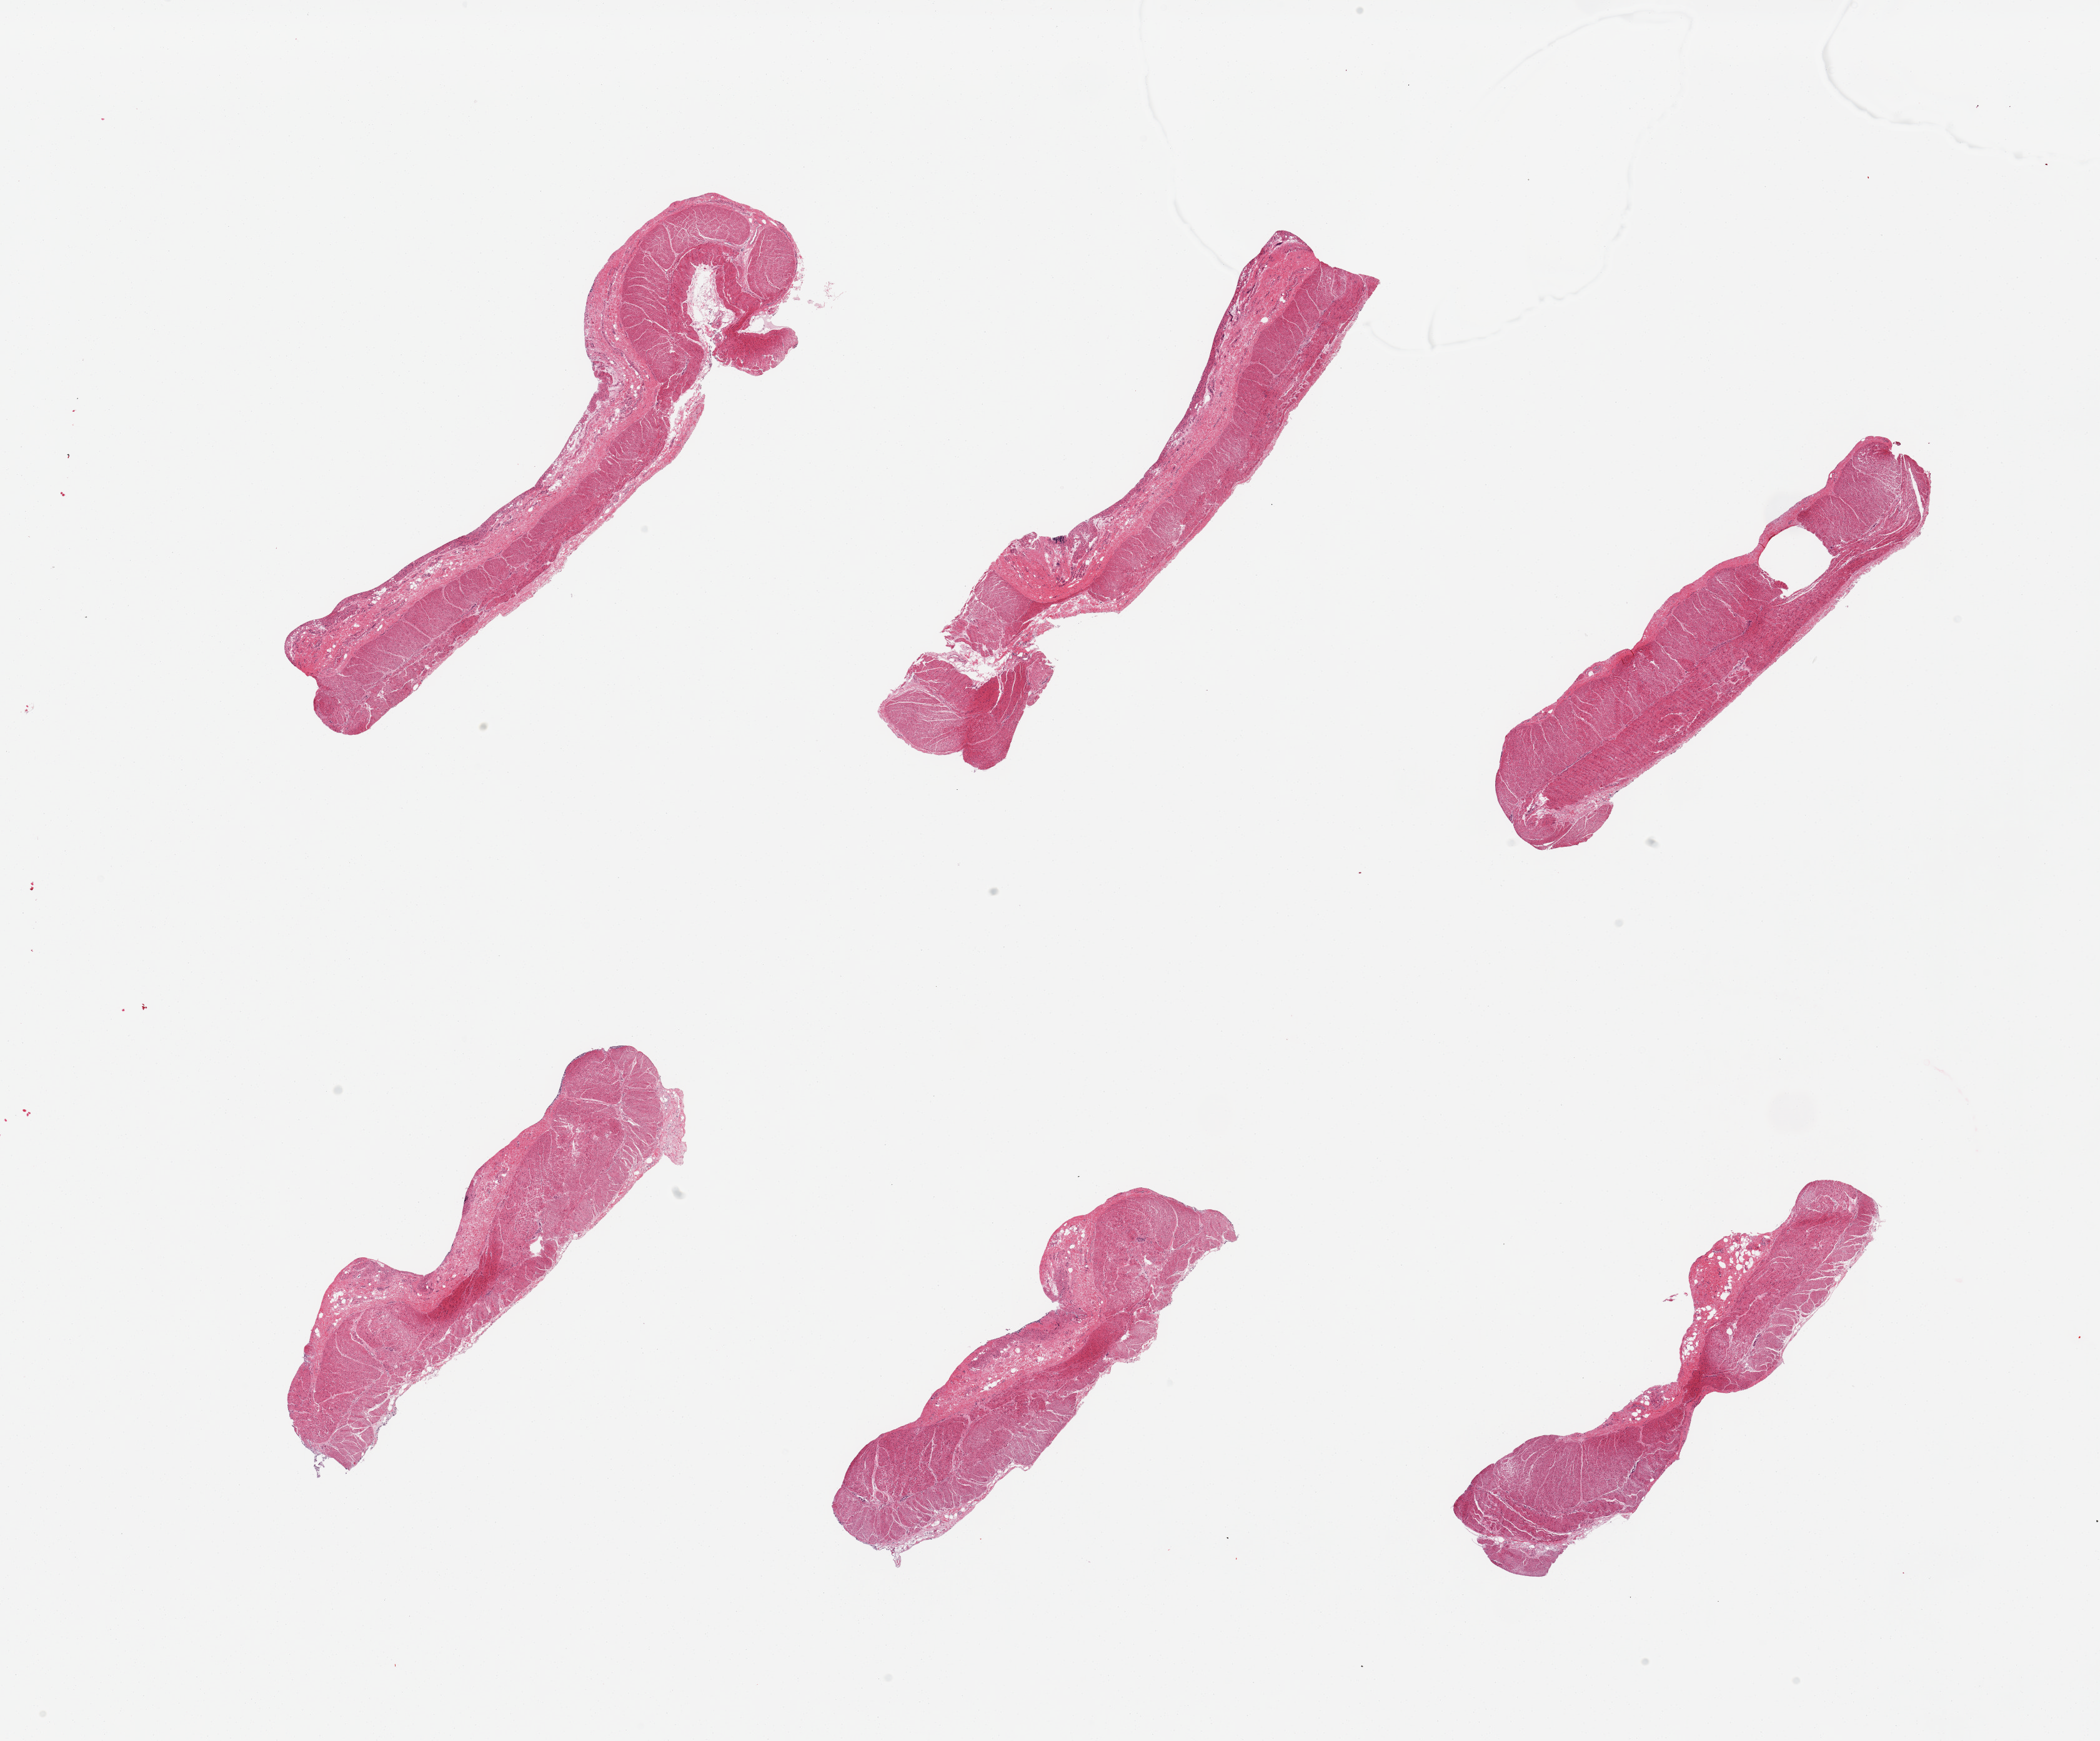
Whole-slide image, haematoxylin and eosin stain — shown as a low-resolution overview of the whole scanned area (about 26.6 x 22.0 mm, from a 20x scan). PAXgene-fixed, paraffin-embedded tissue. Target tissue: sigmoid colon. Donor tissue sample.
Reviewer comment on this tissue sample: 6 pieces; essentially well trimmed muscle.